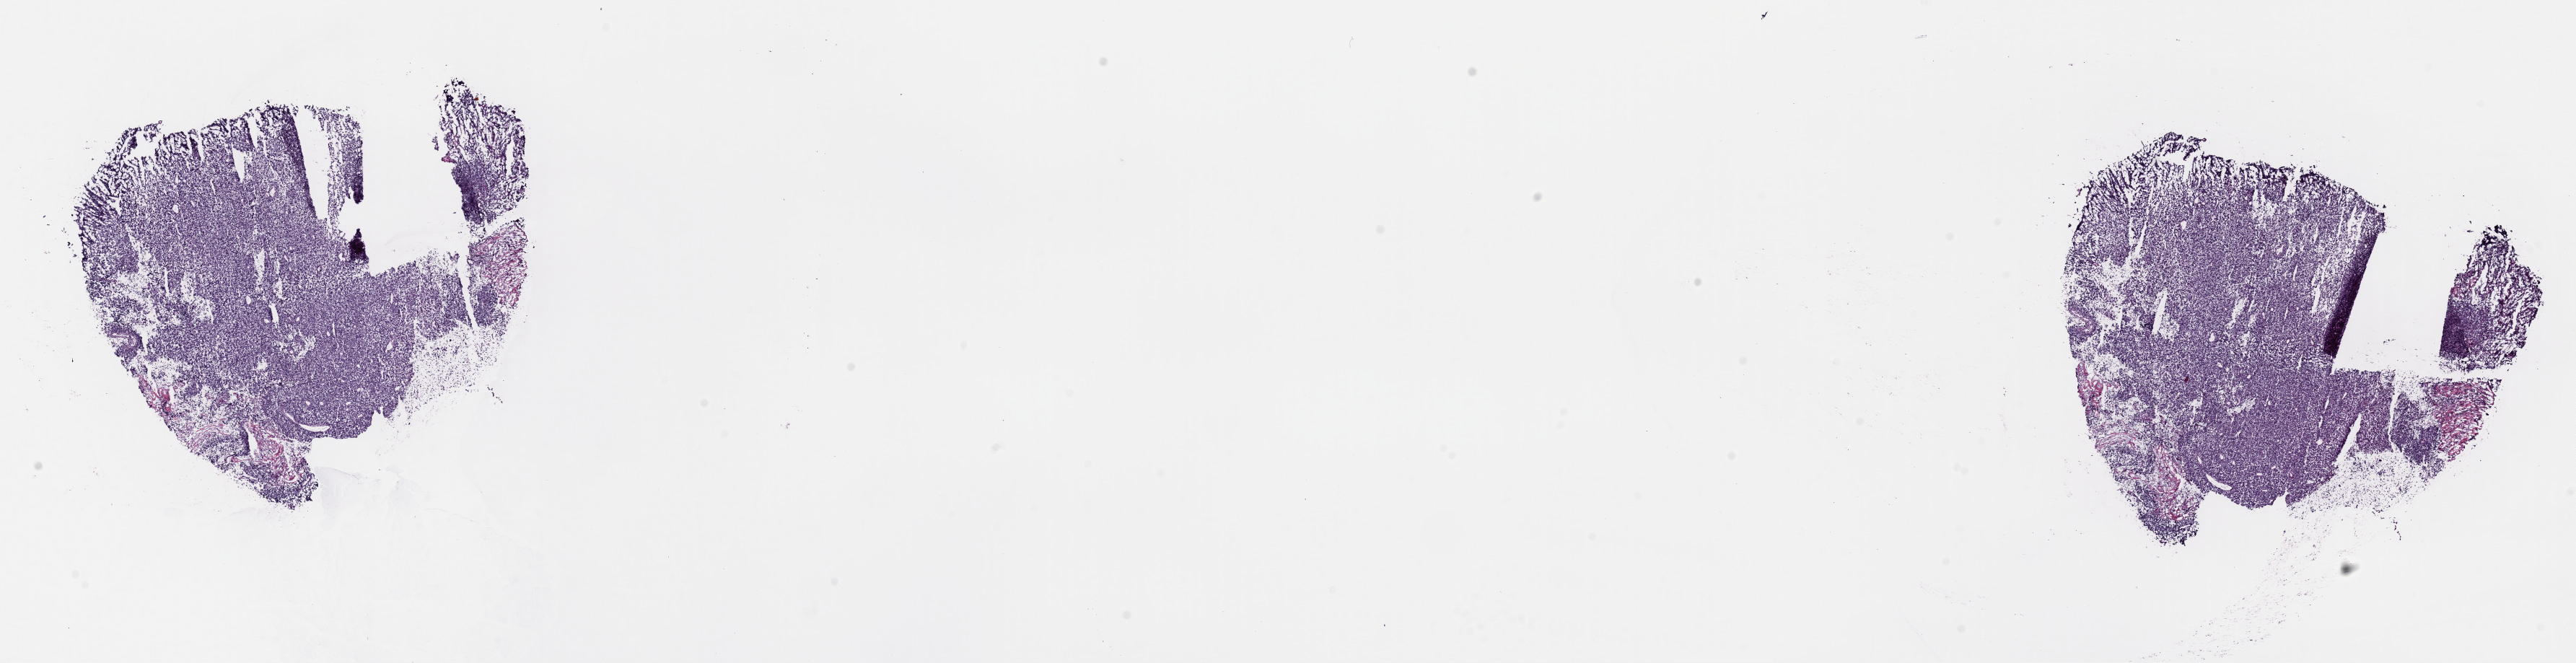
Digitized H&E-stained tissue section (whole slide) — shown as a low-resolution overview of the whole scanned area (about 28.2 x 7.3 mm, acquisition: 40x scan). Frozen section from the top of the tissue portion. Metastatic tumour sample, sampled site: lymph node. Female patient; age at initial diagnosis 71 years. Slide review estimates, as recorded: tumour cells 100%, tumour nuclei 95%, normal cells 0%, stromal cells 0%, necrosis 0%. Inflammatory infiltration, as recorded: lymphocyte infiltration 0%, monocyte infiltration 0%, neutrophil infiltration 0%.
- this section: metastatic tumour tissue
- patient diagnosis: Malignant melanoma, NOS